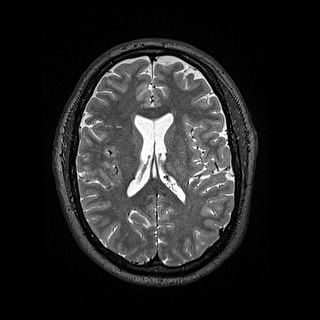
Brain MRI from a brain-tumour surgery series, one axial slice. Position 72 of 144 along the scan axis. 320 × 320 image matrix. From the clinical record (not read from this slice): histopathology: Astrocytoma; WHO grade: 2; IDH mutation: yes; tumour location: Left Insular.
Structures marked on this image (manually delineated by an expert):
- tumour: bounding box (x1, y1, x2, y2) in pixels: (198, 162, 205, 166)